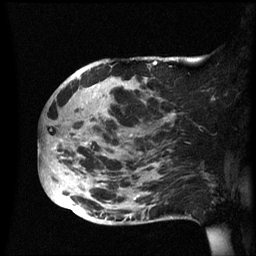
Breast MRI (dynamic contrast-enhanced), one sagittal slice; slice 24 of 60 in the series (ordered by position); dynamic contrast-enhanced series, image 2 of 3 at this slice position (ordered by acquisition); 1.5 T; TE 4.2 ms, TR 8.4 ms; 256 × 256 image matrix. Patient: female, 49 years.
Annotated regions visible in this slice (semi-automatic segmentation, software-assisted and operator-edited):
- analysis volume of interest (the breast-tissue region the enhancement analysis was run in; not a lesion): box from (x=39, y=57) to (x=174, y=225) px
- tumour enhancement mask (voxels above the 70 % enhancement threshold inside the analysis volume of interest): (x=78, y=61)–(x=157, y=79)